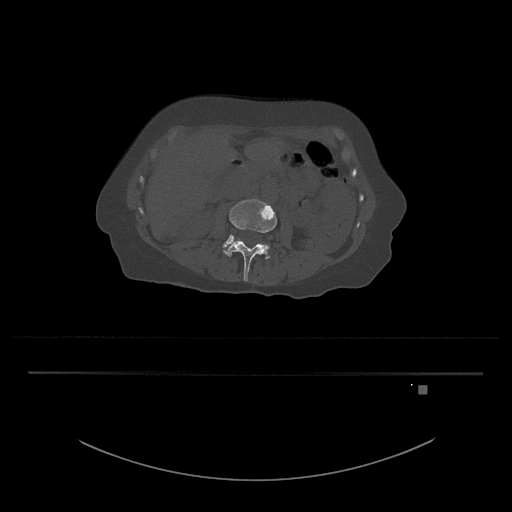
CT including the spine, one axial slice. Position 415 of 797 along the scan axis. Reconstruction kernel Br40s/3. Bone window (W 1800 / L 400 HU). 0.5 mm slice thickness. 512 × 512 image matrix, field of view 500 × 500 mm. Patient: female, 57 years. Case-level facts recorded for this patient, not image findings: primary cancer: cervical.
Annotated regions visible in this slice (semi-automatically segmented with operator editing):
- L3 vertebra: box from (x=223, y=199) to (x=277, y=281) px
- L4 vertebra: (x=222, y=234)–(x=270, y=257)